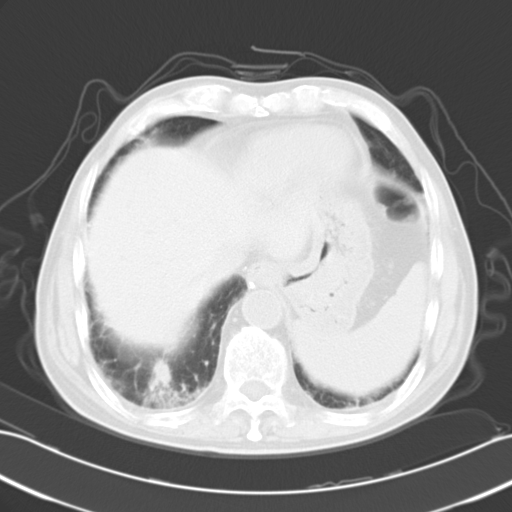
Chest CT, one axial slice; slice 6 of 26 in the series (ordered by position); reconstruction kernel B40f; 120 kVp; lung window (W 1500 / L -600 HU); 512 × 512 image matrix, field of view 353 × 353 mm. Male patient, age 73 years. From the clinical record (not read from this slice): clinical TNM (as recorded): T1a N0 M0.
Structures marked on this image (bounding box drawn by a radiologist):
- lung tumour (recorded histology: small cell carcinoma): box from (x=145, y=361) to (x=174, y=391) px